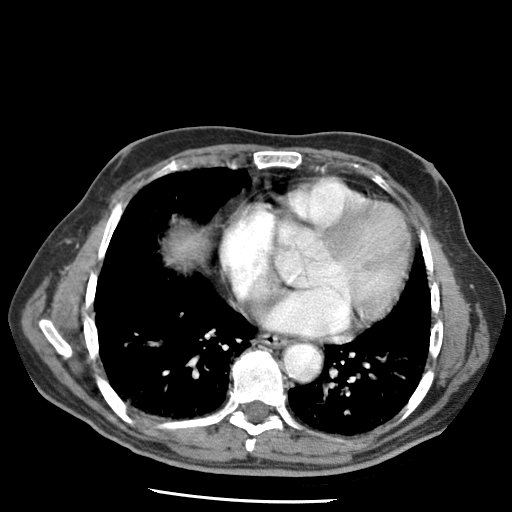
Contrast-enhanced abdominal CT (liver protocol), one axial slice; slice 69 of 79 in the series (ordered by position); reconstruction kernel STANDARD; 120 kVp; soft-tissue window (W 400 / L 40 HU); 2.5 mm slice thickness; 512 × 512 image matrix, field of view 320 × 320 mm. From the clinical record (not read from this slice): diagnosis: hepatocellular carcinoma (patient treated with transarterial chemoembolisation; whether this scan precedes or follows treatment is not stated here); TNM stage (as recorded): Stage-IIIA; Child-Pugh class: A; tumour differentiation: moderately differentiated.
Outlined on this slice (semi-automatically segmented with operator editing):
- liver parenchyma outside the tumour (the mass and vessels are separate outlines, so this box may not span the whole liver): bounding box <170,232,206,262> (left, top, right, bottom; pixels)